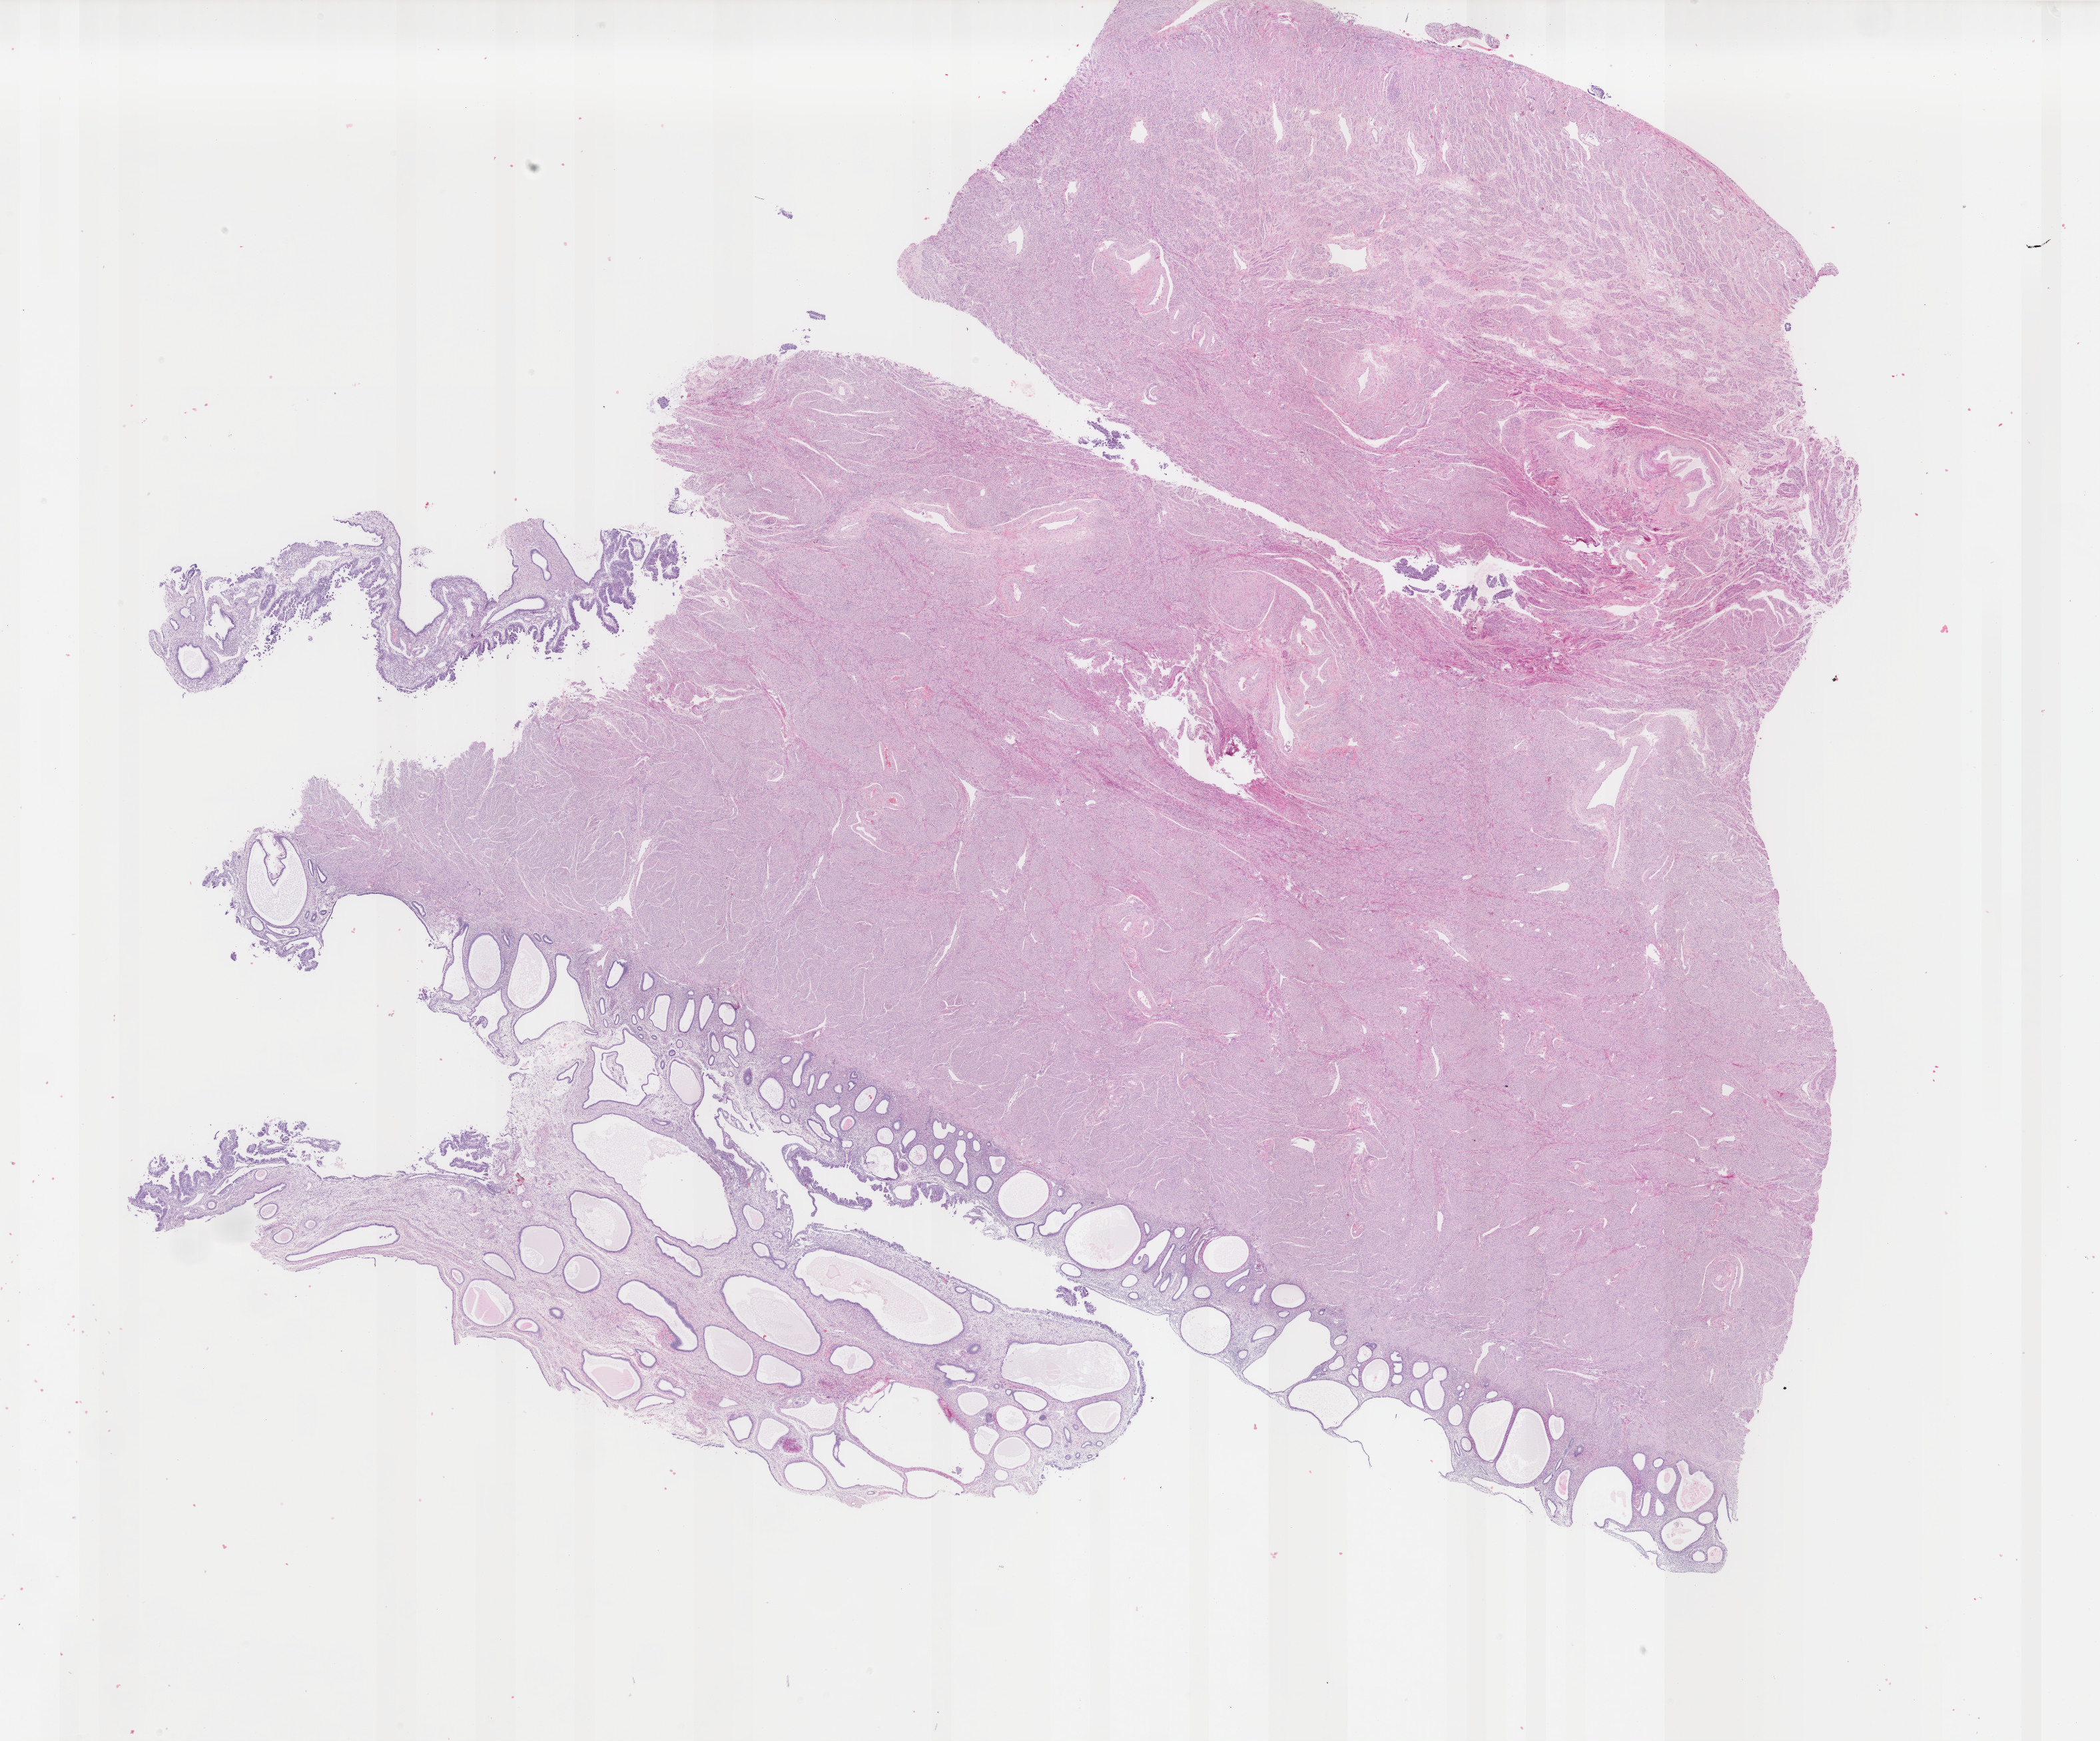
Whole-slide histology image, H&E, shown as a low-resolution overview of the whole scanned area (about 25.0 x 20.7 mm, from a 40x scan); formalin-fixed paraffin-embedded (FFPE) diagnostic section; sample: primary tumour, uterus. Female patient.
Pathologic diagnosis: Serous cystadenocarcinoma, NOS (endometrium).